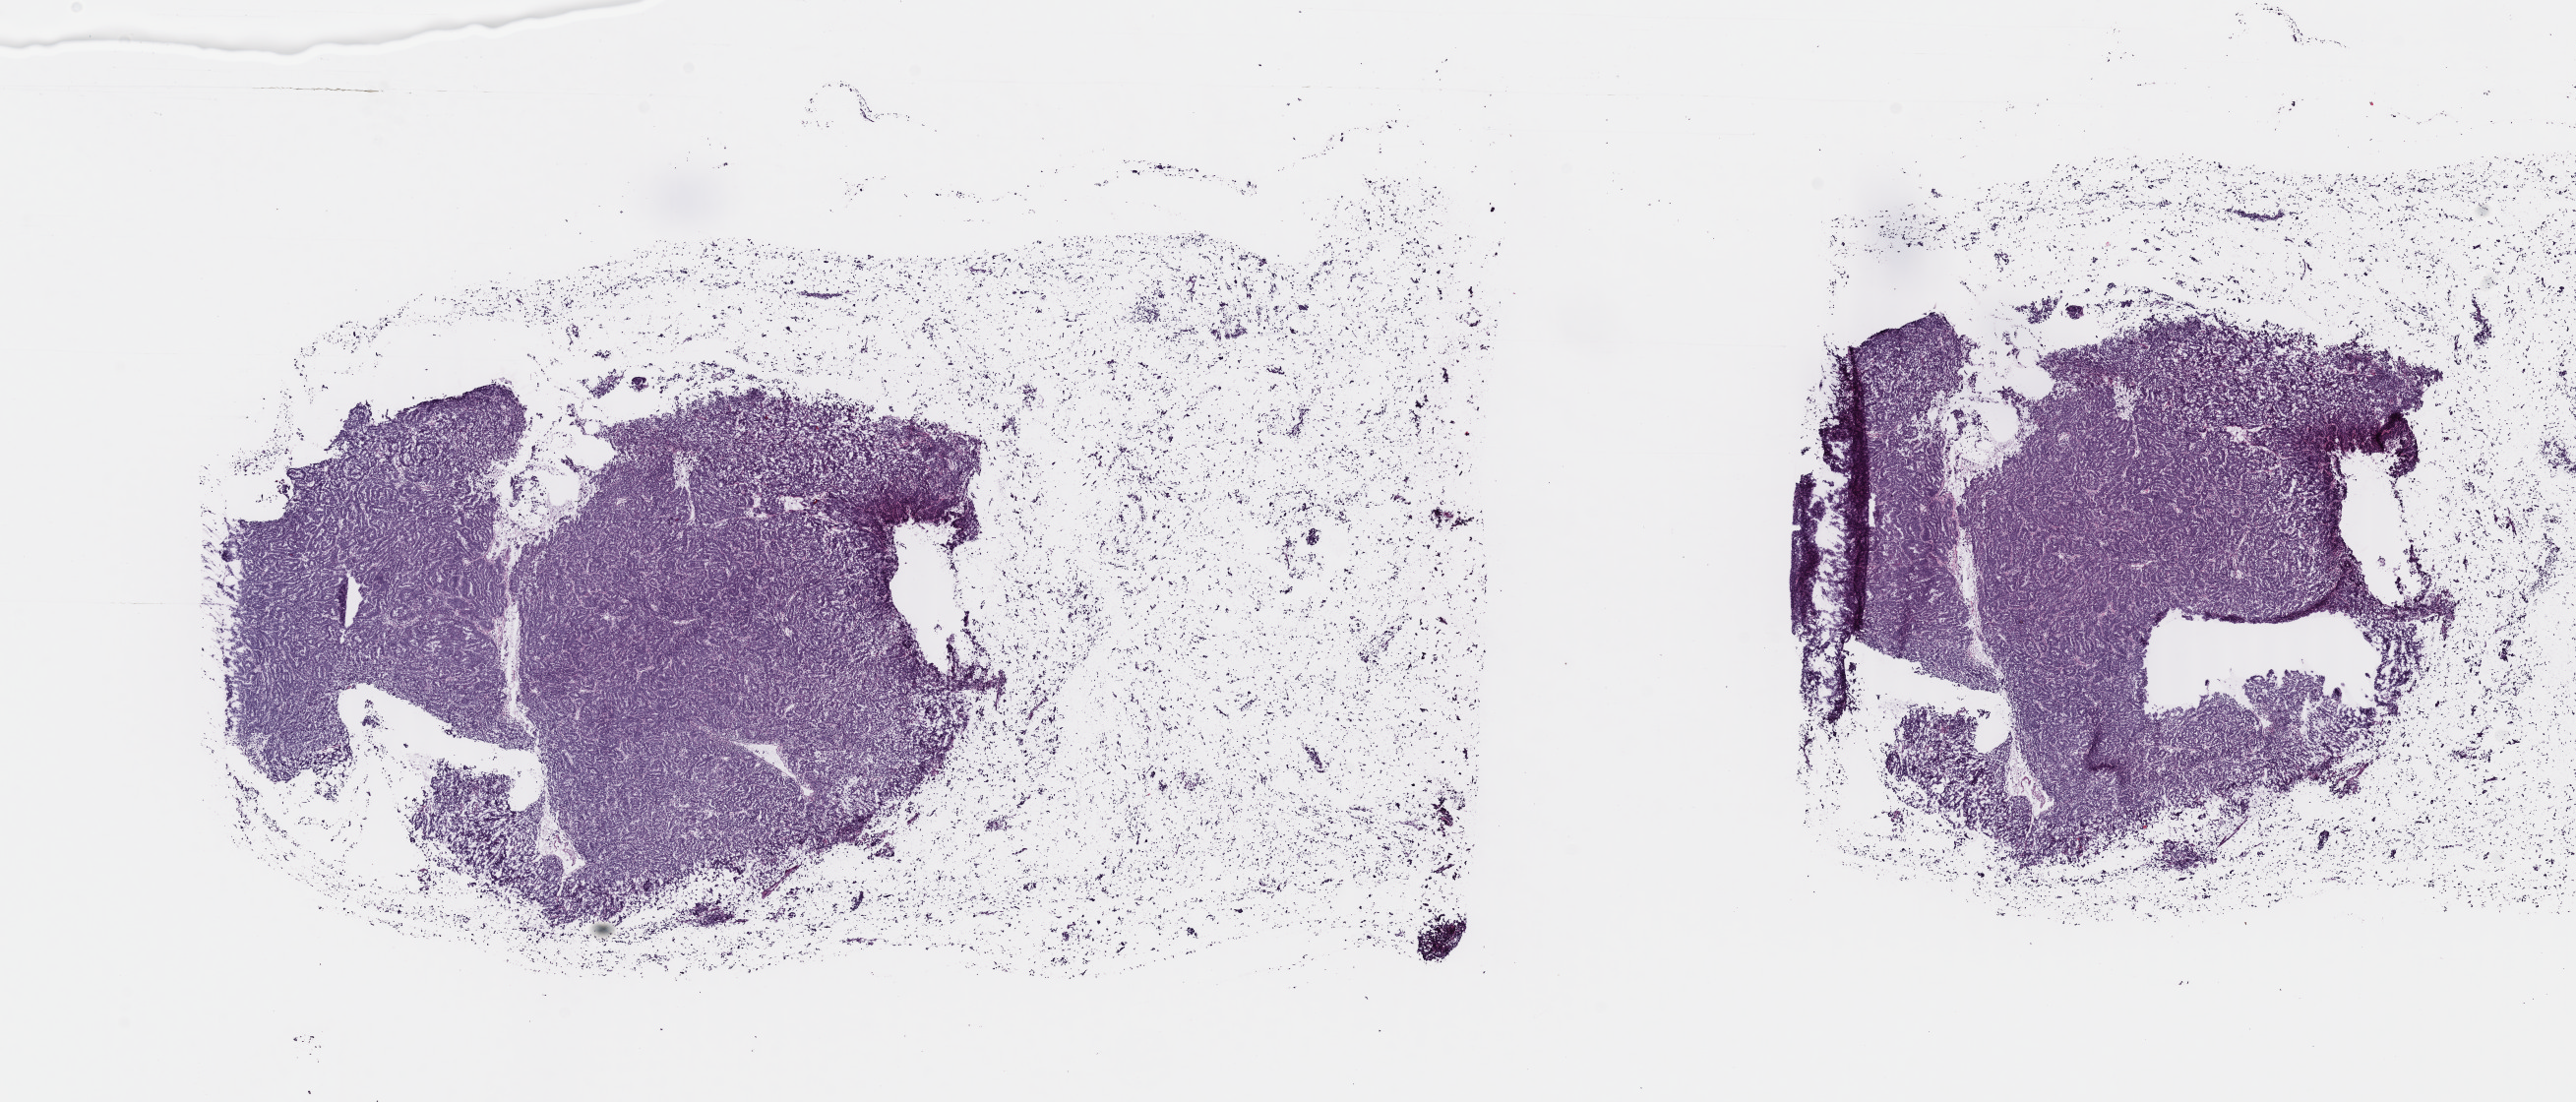
Whole-slide histology image, Hematoxylin and eosin (H&E) stained — shown as a low-resolution overview of the whole scanned area (about 20.7 x 8.8 mm). Frozen section. Uterus, primary tumour sample. Female, age 82 years at initial diagnosis. Histologic grade: G3 (poorly differentiated). Slide review estimates, as recorded: tumour cells 95%, tumour nuclei 95%, normal cells 0%, stromal cells 5%, necrosis 0%. Infiltration values recorded for this section: lymphocyte infiltration 35%, monocyte infiltration 5%, neutrophil infiltration 15%.
* pathologic diagnosis: Serous cystadenocarcinoma, NOS
* FIGO stage: IIIC2